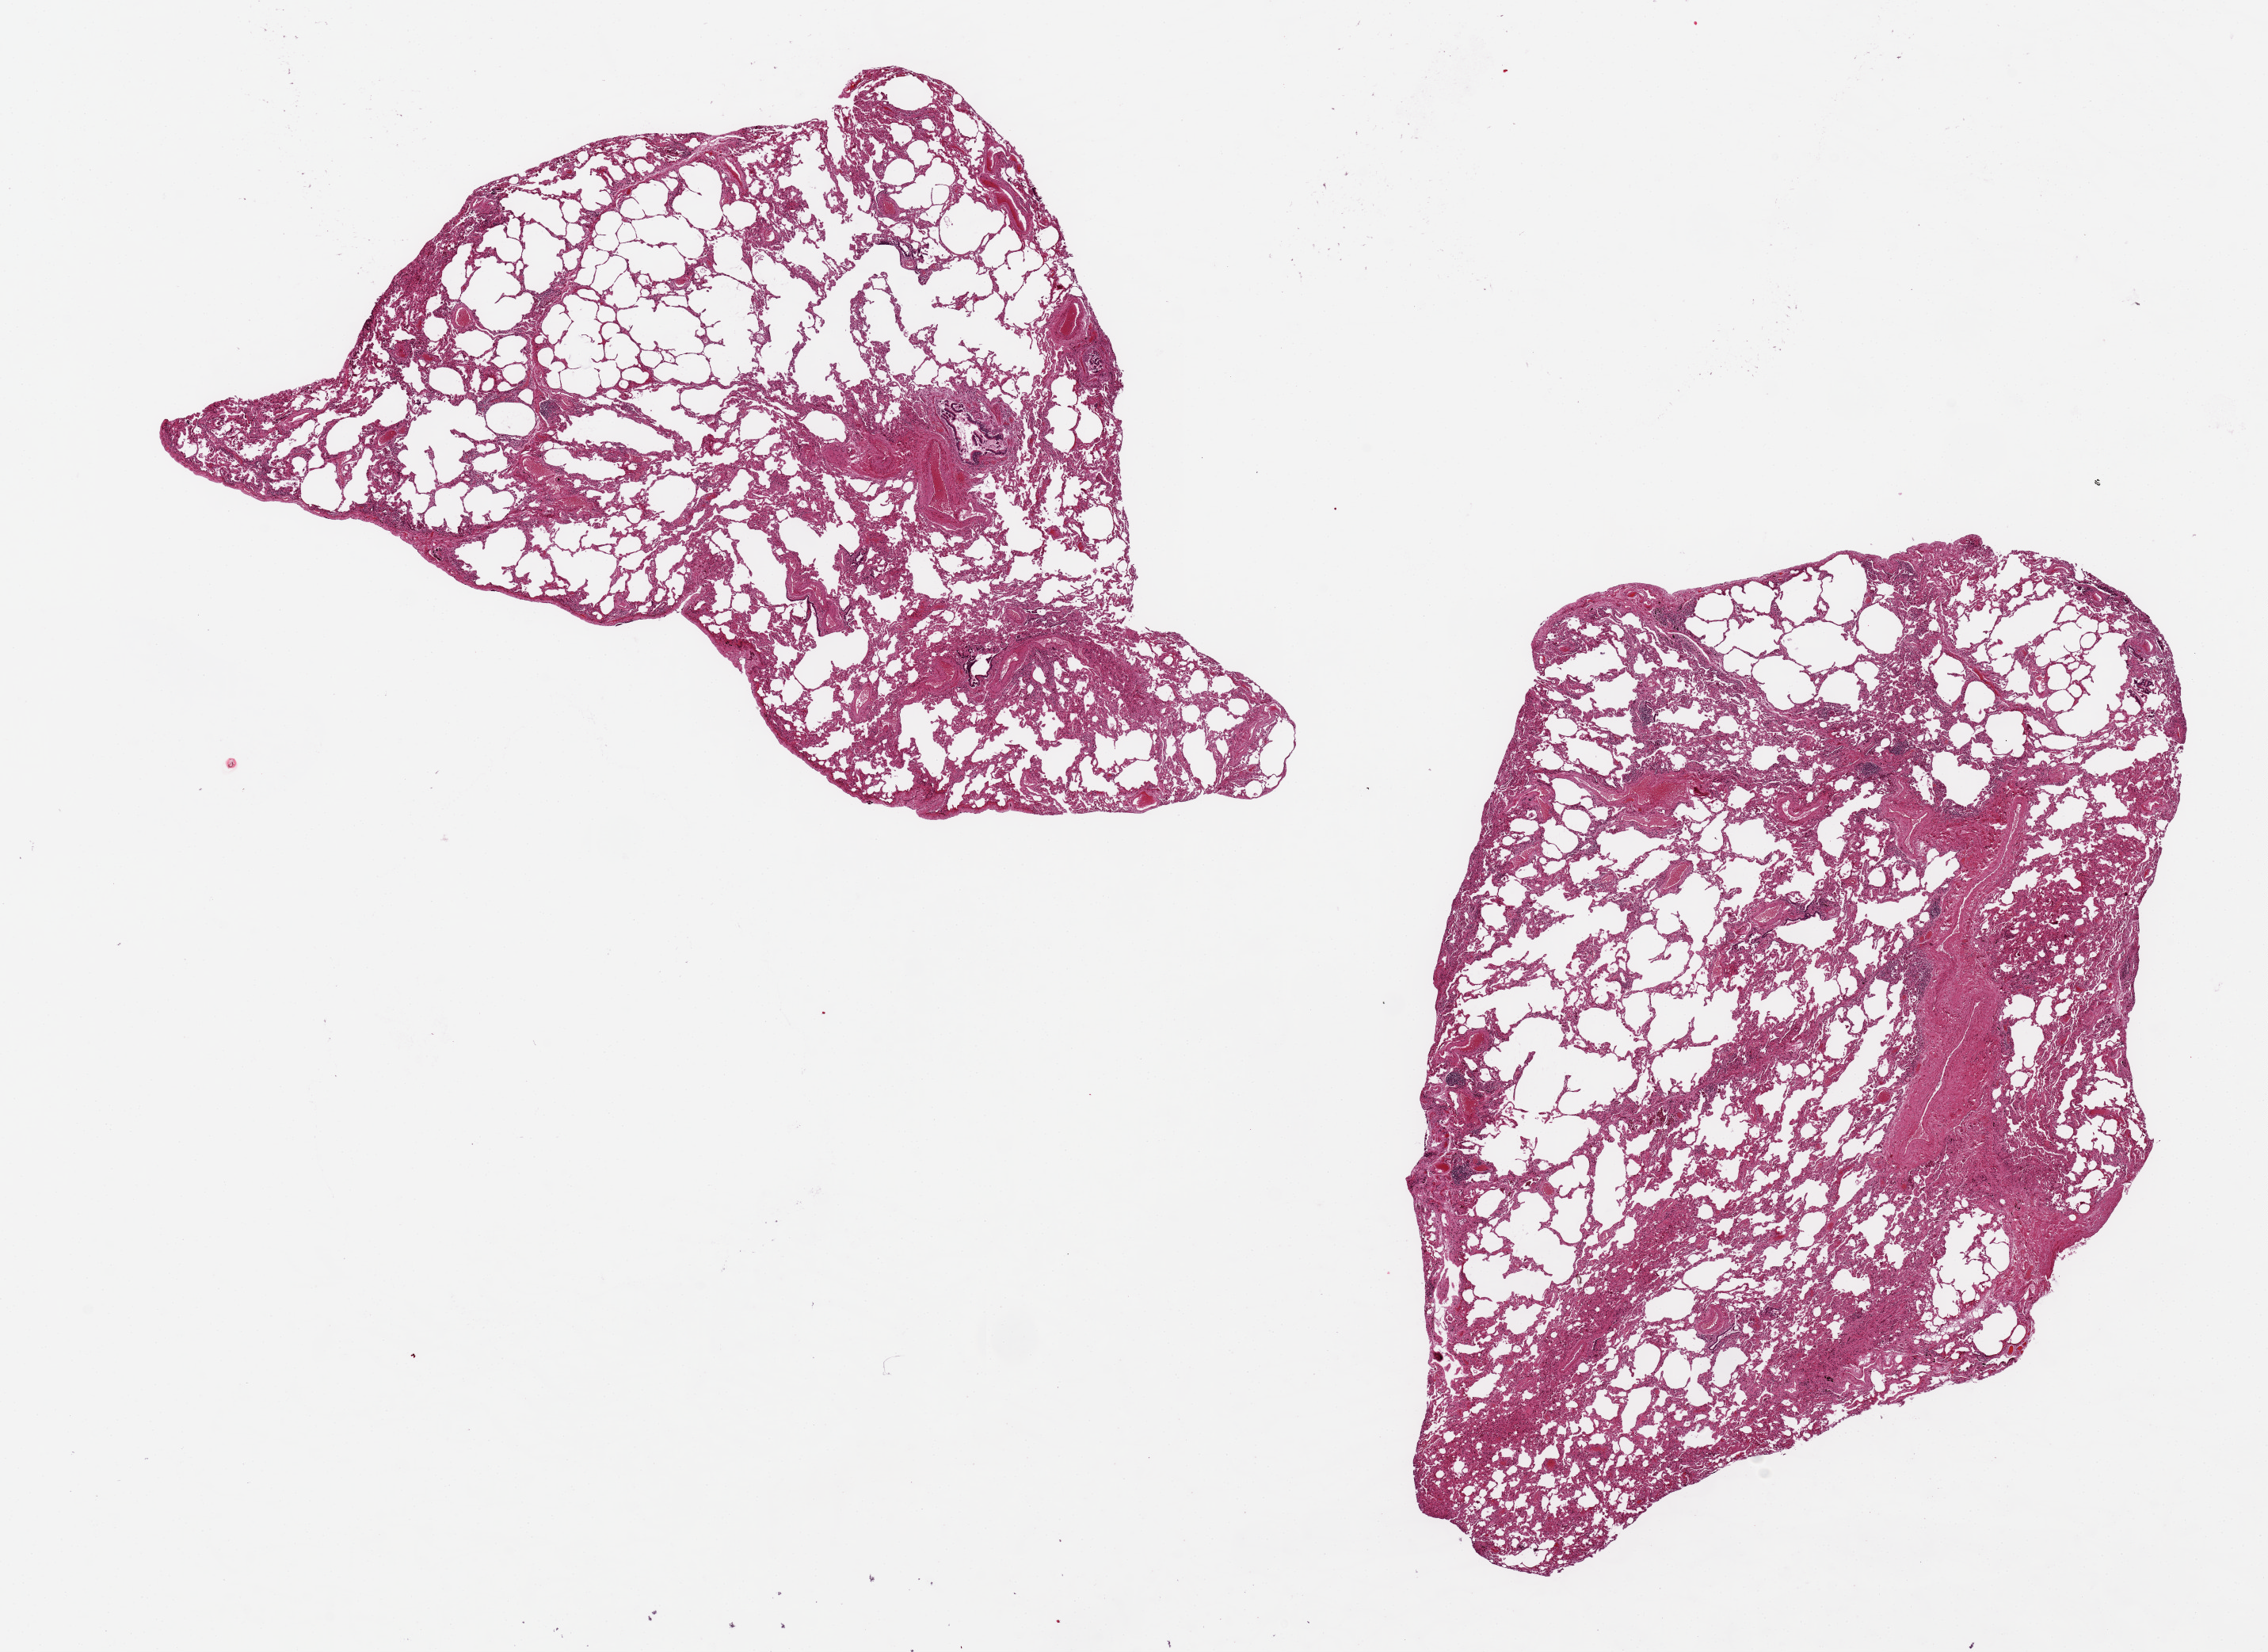
Digitized hematoxylin and eosin (H&E)-stained section, brightfield, shown as a low-resolution overview of the whole scanned area (about 22.6 x 16.5 mm, acquisition: 20x scan). PAXgene-fixed, paraffin-embedded tissue. Sampled site (target tissue): lung. Tissue donor sample. Donor: male.
* reviewer comment on this tissue sample: 2 aliquots, 10x 7mm, foci of chronic inflammation--areas of emphysematous damage